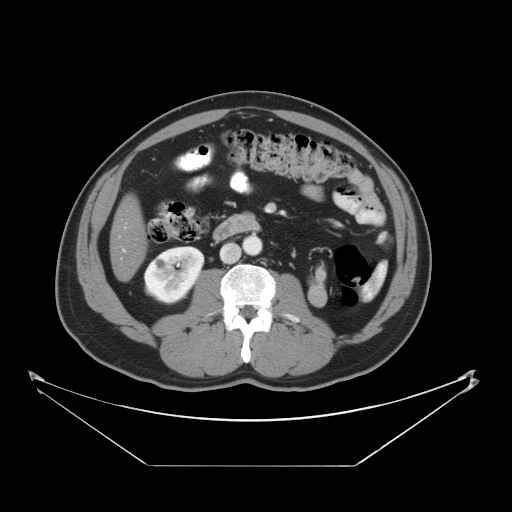
Contrast-enhanced abdominal CT, one axial slice. Slice 12 of 46 in the series (ordered by position). Reconstruction kernel STANDARD. Intravenous contrast given. Soft-tissue window (W 400 / L 40 HU). 5 mm slice thickness. 512 × 512 image matrix, field of view 465 × 465 mm. Male patient, age 57 years. Case-level facts recorded for this patient, not image findings: diagnosis: colorectal cancer liver metastases, imaged before liver resection; multiple liver metastases: no; largest metastasis: 3.3 cm.
Structures marked on this image (expert manual segmentation):
- liver: box from (x=112, y=199) to (x=144, y=280) px
- planned liver remnant (the part of the liver to remain after resection): (x=112, y=199)–(x=144, y=279)